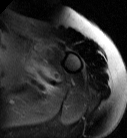
MRI of an extremity soft-tissue mass, one axial slice. Slice 64 of 87 in the series (ordered by position). T2-weighted fat-saturated. MR volume resampled by the dataset authors to the PET/CT grid (not the native acquisition matrix). 3.27 mm slice thickness. 127 × 138 image matrix, field of view 124 × 135 mm. Female patient. From the clinical record (not read from this slice): histological type: pleiomorphic leiomyosarcoma; grade: high; site of the primary tumour: left biceps.
Structures marked on this image (expert contour drawn on MRI and transferred to this co-registered scan by the dataset authors):
- gross tumour volume including surrounding oedema: bounding box <33,46,53,70> (left, top, right, bottom; pixels)